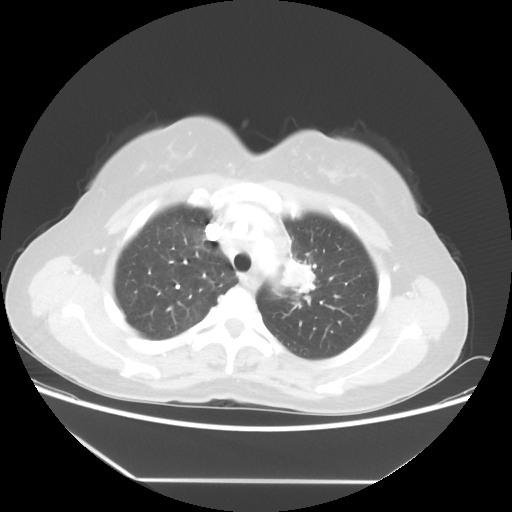
Chest CT, one axial slice. Slice 41 of 52 in the series (ordered by position). Reconstruction kernel STANDARD. 100 kVp. Lung window (W 1500 / L -600 HU). 5 mm slice thickness. 512 × 512 image matrix, field of view 390 × 390 mm. Patient: female, 50 years. Case-level facts recorded for this patient, not image findings: clinical TNM (as recorded): T2 N3 M0.
Structures marked on this image (bounding box drawn by a radiologist):
- lung tumour (recorded histology: adenocarcinoma): bounding box (x1, y1, x2, y2) in pixels: (278, 248, 319, 301)